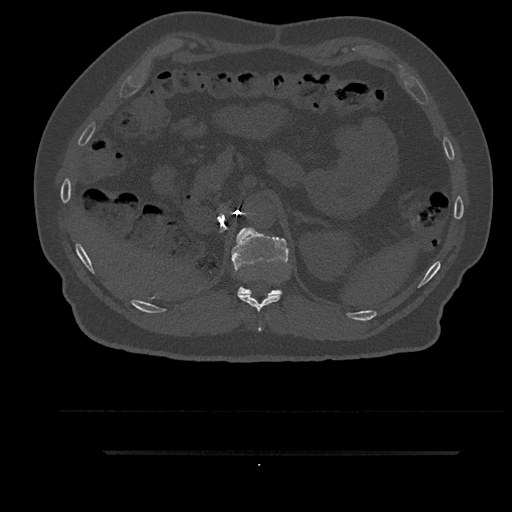
CT including the spine, one axial slice; position 273 of 797 along the scan axis; 120 kVp; bone window (W 1800 / L 400 HU); 0.5 mm slice thickness; 512 × 512 image matrix, field of view 432 × 432 mm. Male patient, age 63 years. From the clinical record (not read from this slice): primary cancer: renal; vertebrae with lytic lesions (as recorded): T8.
Annotated regions visible in this slice (semi-automatic segmentation, software-assisted and operator-edited):
- T11 vertebra: bounding box [x1, y1, x2, y2] px = [238, 294, 282, 332]
- T12 vertebra: [231, 227, 289, 295]